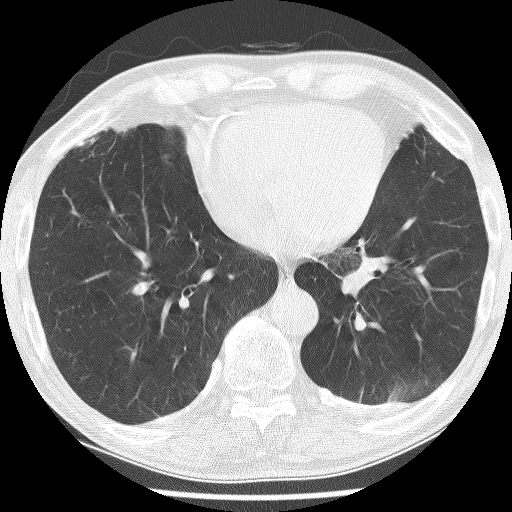
Chest CT (low-dose screening protocol), one axial image, baseline annual screen, lung window (W 1500 / L -600 HU), lung (sharp) reconstruction kernel (BONE), 120 kVp, slice 165 of 226 in the series. Male participant, aged 74 years at enrolment. Current smoker at enrolment.
Expert-annotated lung lesion, bounding box [x1, y1, x2, y2] px = [319, 232, 428, 326]. Screening reader's record for this exam (one nodule recorded; not confirmed to be the boxed lesion): non-calcified nodule or mass ≥4 mm, left lower lobe, 30 × 27 mm, spiculated (stellate) margins, soft tissue attenuation. Official screen result: positive, change unspecified: nodule(s) >= 4 mm or enlarging nodule(s), mass(es), or other non-specific abnormalities suspicious for lung cancer. Participant outcome: lung cancer diagnosed 151 days after this screen — adenocarcinoma, NOS, left lower lobe, stage IIIA (AJCC 6th edition), 49 mm at pathology.